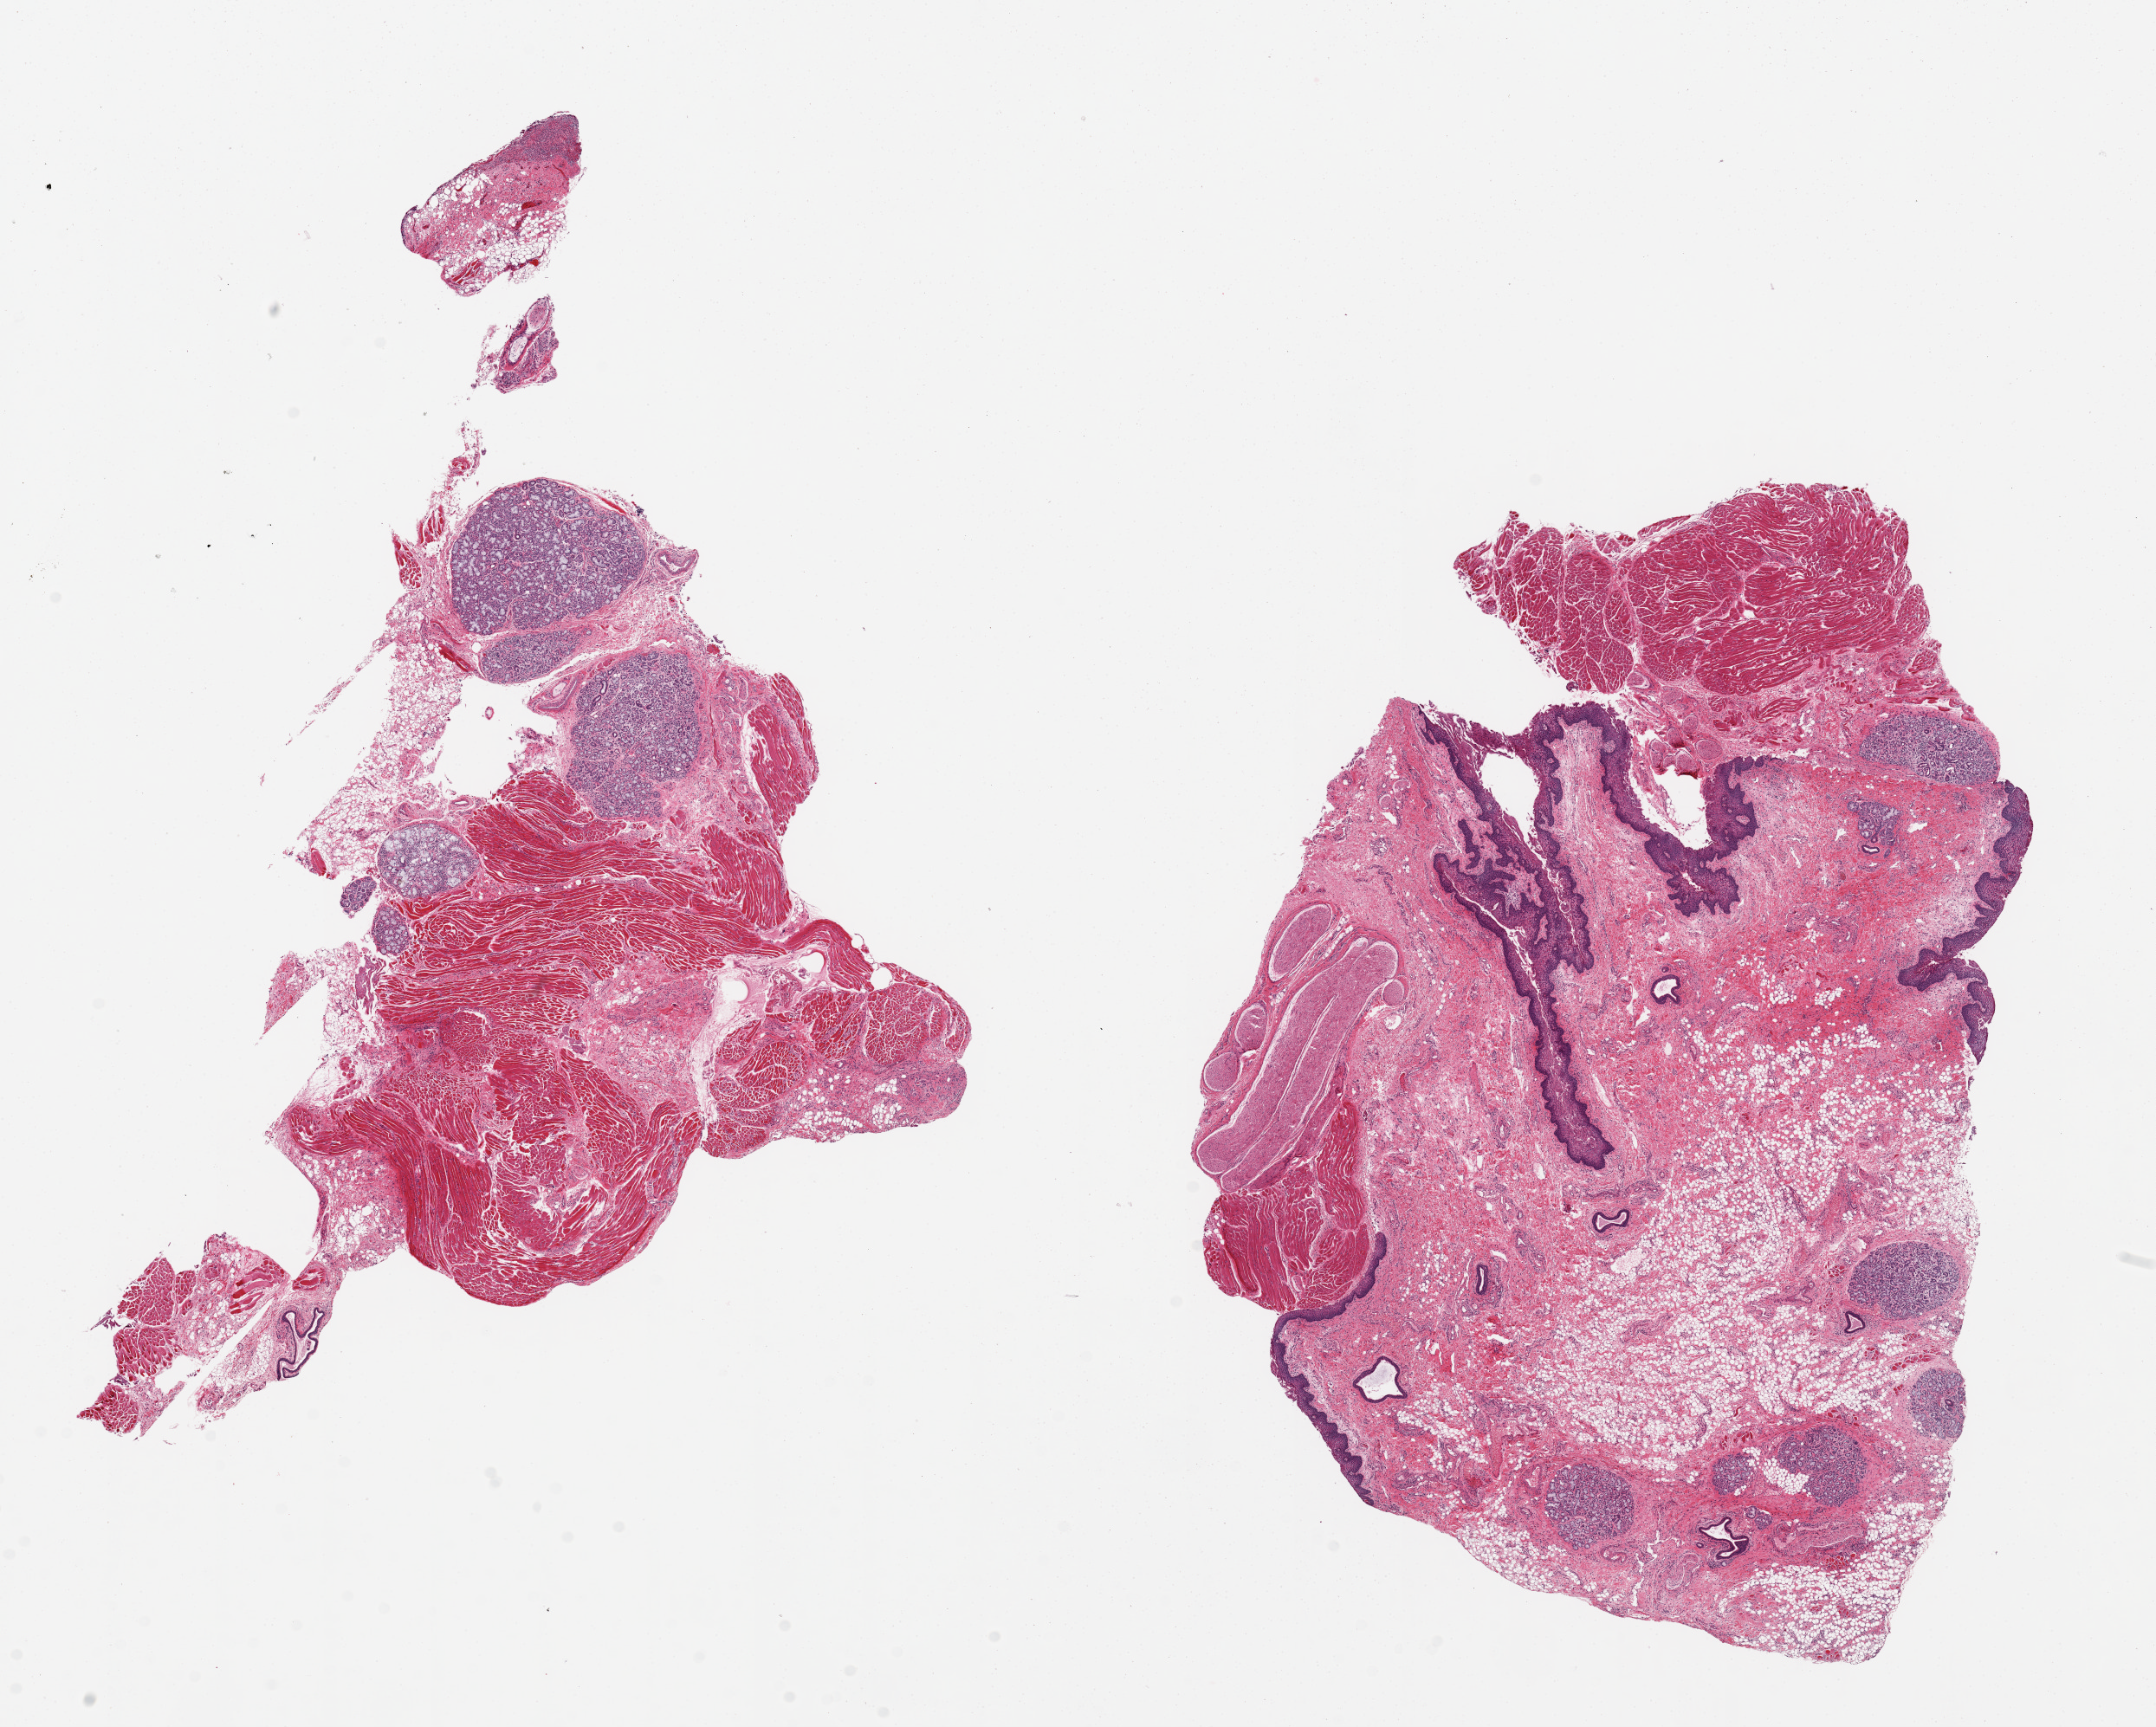
Haematoxylin and eosin whole-slide image, shown as a low-resolution overview of the whole scanned area (about 19.7 x 15.8 mm, slide scanned at 20x); PAXgene-fixed, paraffin-embedded tissue; section of minor salivary gland (target tissue); donor tissue sample. Female donor.
- pathologist's review note for this sample: 2 pieces glandular tissue is ~10-15% of both sections, rest is squamous mucosa and fibromuscular and adipose tissue